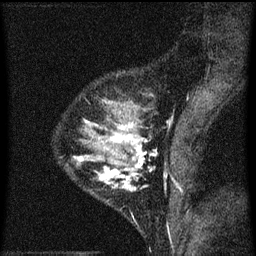
Breast MRI (dynamic contrast-enhanced), one sagittal slice. Slice 20 of 60 in the series (ordered by position). Dynamic contrast-enhanced series, image 2 of 3 at this slice position (ordered by acquisition). 1.5 T. TE 4.2 ms, TR 8 ms. 2 mm slice thickness. 256 × 256 image matrix, field of view 180 × 180 mm. Female patient, age 33 years.
Outlined on this slice (semi-automatically segmented with operator editing):
- analysis volume of interest (the breast-tissue region the enhancement analysis was run in; not a lesion): bounding box (x1, y1, x2, y2) in pixels: (69, 118, 157, 199)
- tumour enhancement mask (voxels above the 70 % enhancement threshold inside the analysis volume of interest): (76, 122, 152, 191)